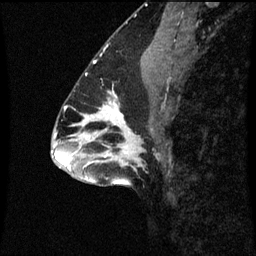
Breast MRI (dynamic contrast-enhanced), one sagittal slice; position 34 of 60 along the scan axis; dynamic contrast-enhanced series, image 2 of 3 at this slice position (ordered by acquisition); 1.5 T; TE 4.2 ms, TR 8.9 ms; 2 mm slice thickness; 256 × 256 image matrix, field of view 200 × 200 mm. Patient: female, 43 years. From the clinical record (not read from this slice): setting: breast cancer imaged before/during neoadjuvant chemotherapy; receptor status: HR-positive, HER2-negative.
Outlined on this slice (semi-automatic segmentation, software-assisted and operator-edited):
- analysis volume of interest (the breast-tissue region the enhancement analysis was run in; not a lesion): box from (x=96, y=96) to (x=155, y=159) px
- tumour enhancement mask (voxels above the 70 % enhancement threshold inside the analysis volume of interest): (x=104, y=96)–(x=123, y=119)